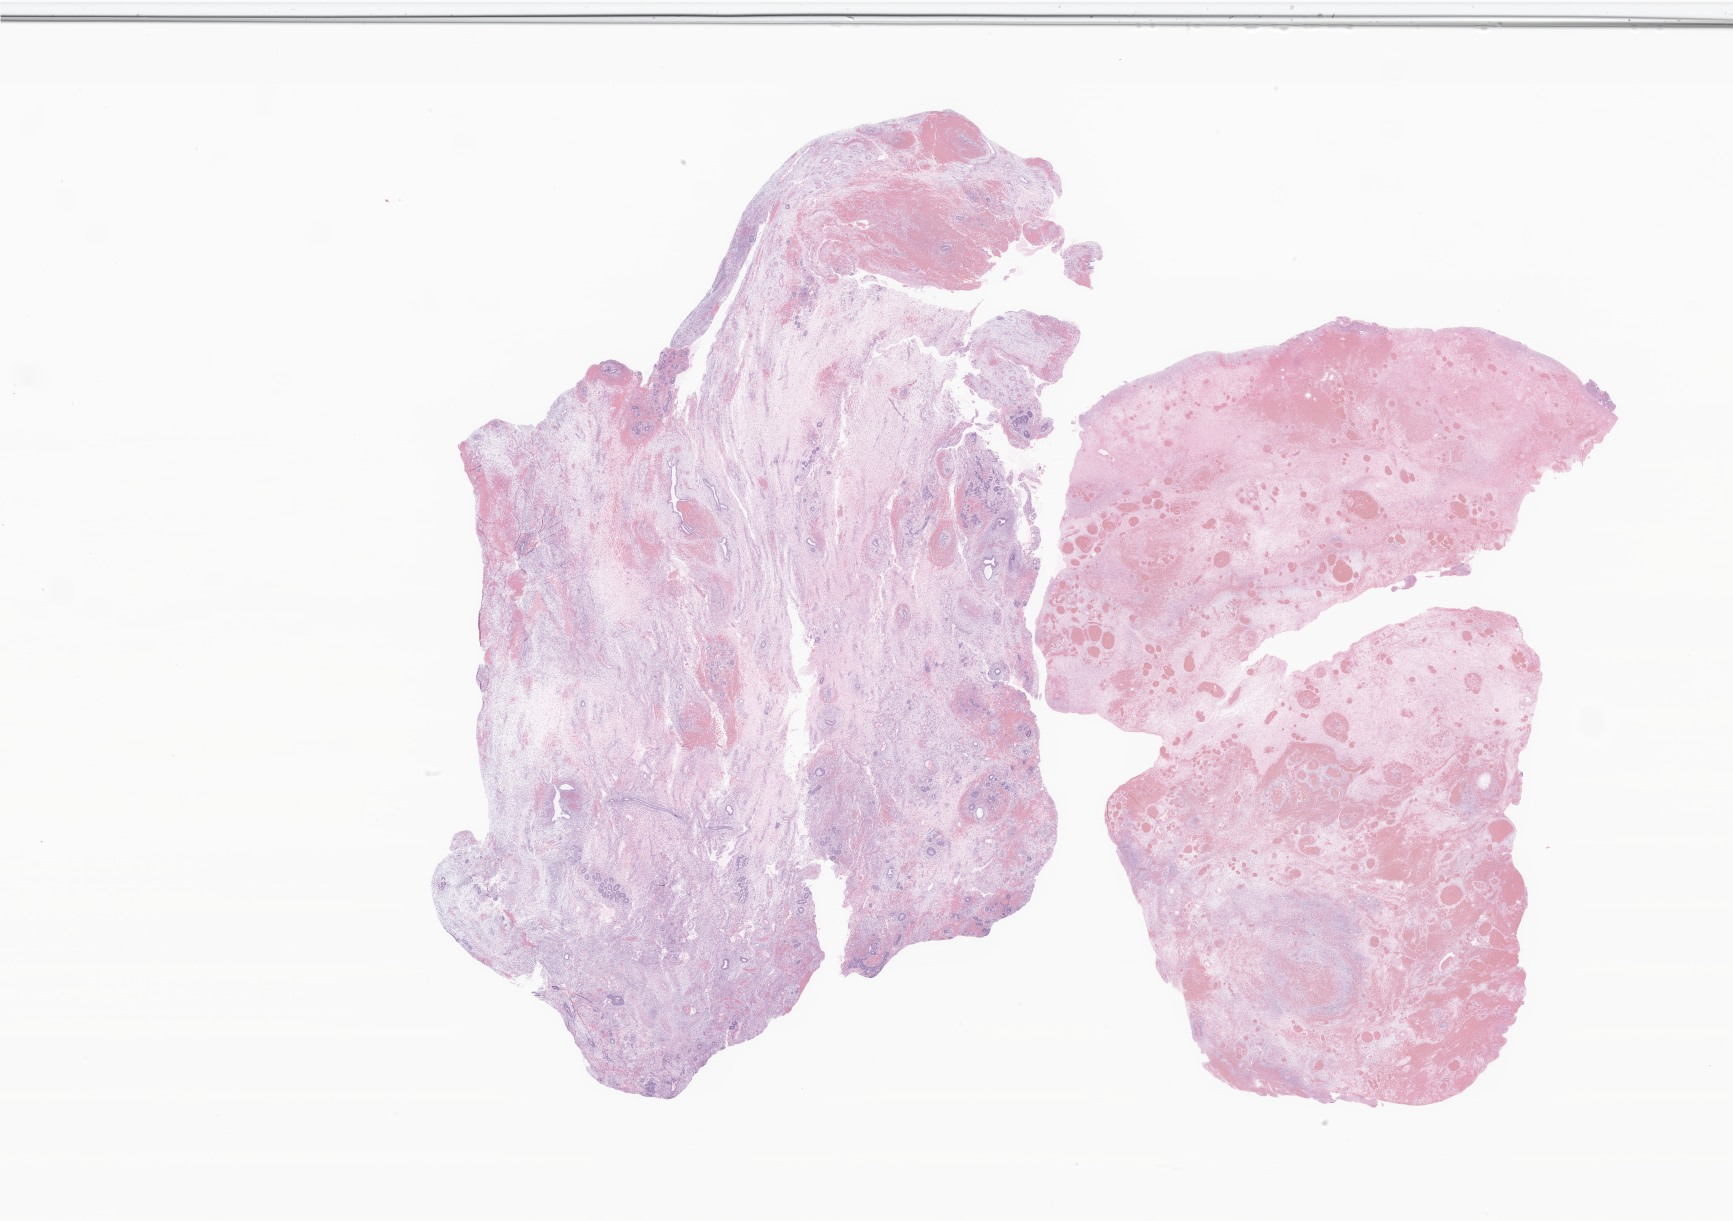
Whole-slide image, haematoxylin and eosin stain of tumor tissue from the uterus, a low-resolution overview of the entire scanned area, about 29.2 x 20.6 mm. FFPE section. Patient: female, age 193 months (16 years 1 month).
Recorded diagnosis: Embryonal rhabdomyosarcoma, NOS.